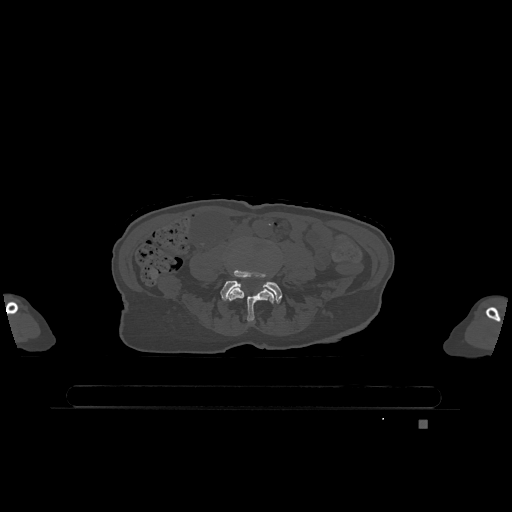
CT including the spine, one axial slice. Position 269 of 1317 along the scan axis. Bone window (W 1800 / L 400 HU). 0.5 mm slice thickness. 512 × 512 image matrix, field of view 500 × 500 mm. Female patient, age 74 years. From the clinical record (not read from this slice): primary cancer: lung; vertebrae with lytic lesions (as recorded): T1, T4, T5, T6, L4, L5.
Structures marked on this image (semi-automatic segmentation, software-assisted and operator-edited):
- L4 vertebra: box from (x=228, y=288) to (x=274, y=322) px
- L5 vertebra: (x=220, y=271)–(x=282, y=303)